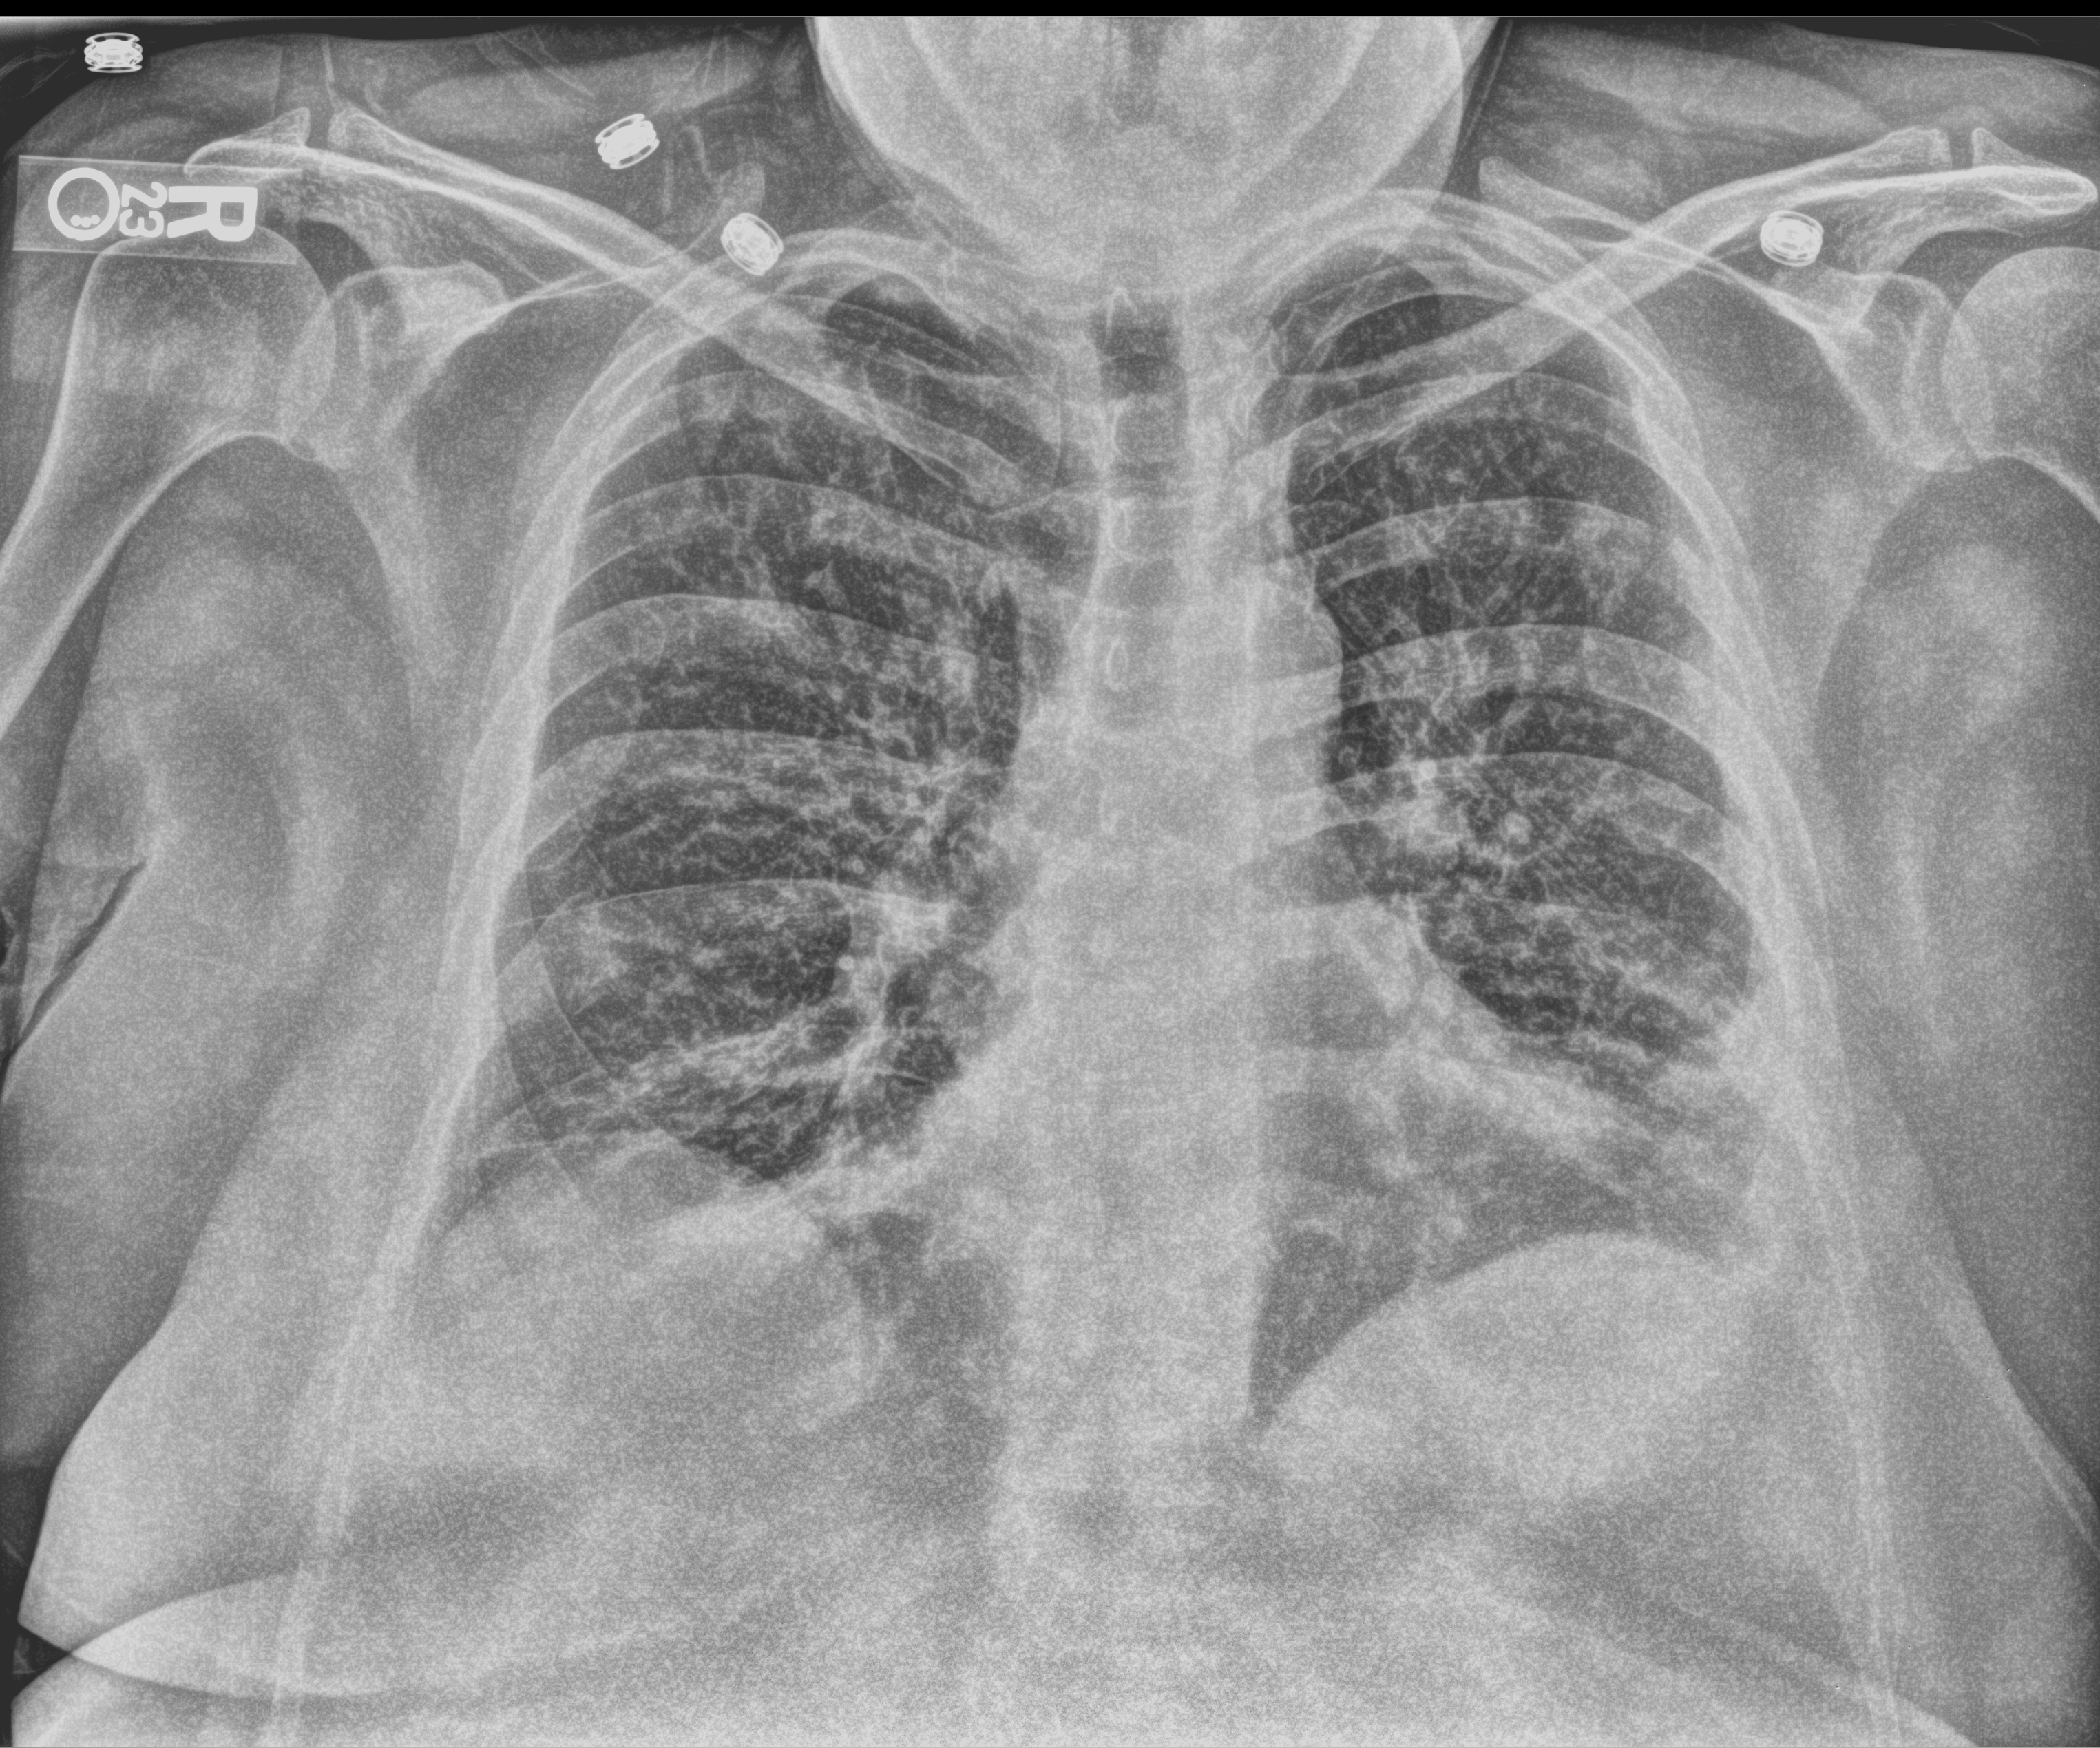
Bedside chest radiograph (computed radiography), anteroposterior (AP) projection. Female patient hospitalised with COVID-19, age 18–59 years.
Admission-level facts for this patient (not findings on this image; timing relative to this image not recorded): length of hospital stay: 10 days.